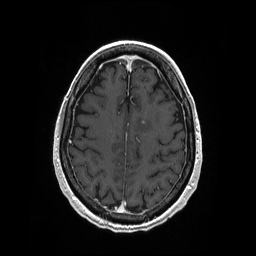
Brain MRI from a brain-tumour surgery series, one axial slice. Slice 68 of 208 in the series (ordered by position). T1-weighted post-contrast. 1 mm slice thickness. 256 × 256 image matrix. Case-level facts recorded for this patient, not image findings: histopathology: Primary diffuse large B-cell lymphoma; tumour location: Left Corpus Callosum (Frontal).
Outlined on this slice (manually delineated by an expert):
- tumour: box from (x=142, y=121) to (x=145, y=124) px